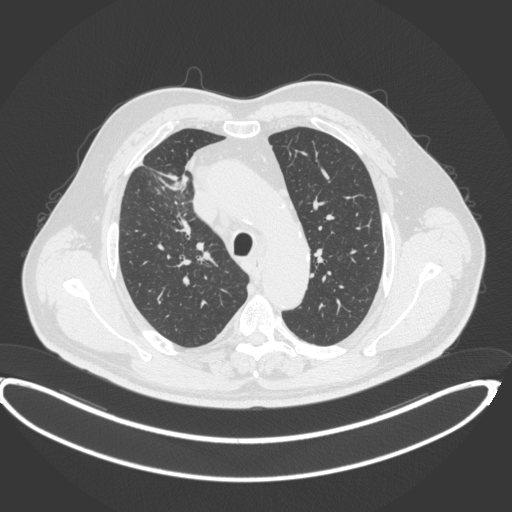
Chest CT, one axial slice. Slice 305 of 395 in the series (ordered by position). Reconstruction kernel B31f. 120 kVp. Lung window (W 1500 / L -600 HU). 1 mm slice thickness. 512 × 512 image matrix, field of view 448 × 448 mm. Patient: male, 62 years. From the clinical record (not read from this slice): clinical TNM (as recorded): T1c N3 M1c.
Structures marked on this image (bounding box drawn by a radiologist):
- lung tumour (recorded histology: adenocarcinoma): box from (x=166, y=175) to (x=188, y=193) px